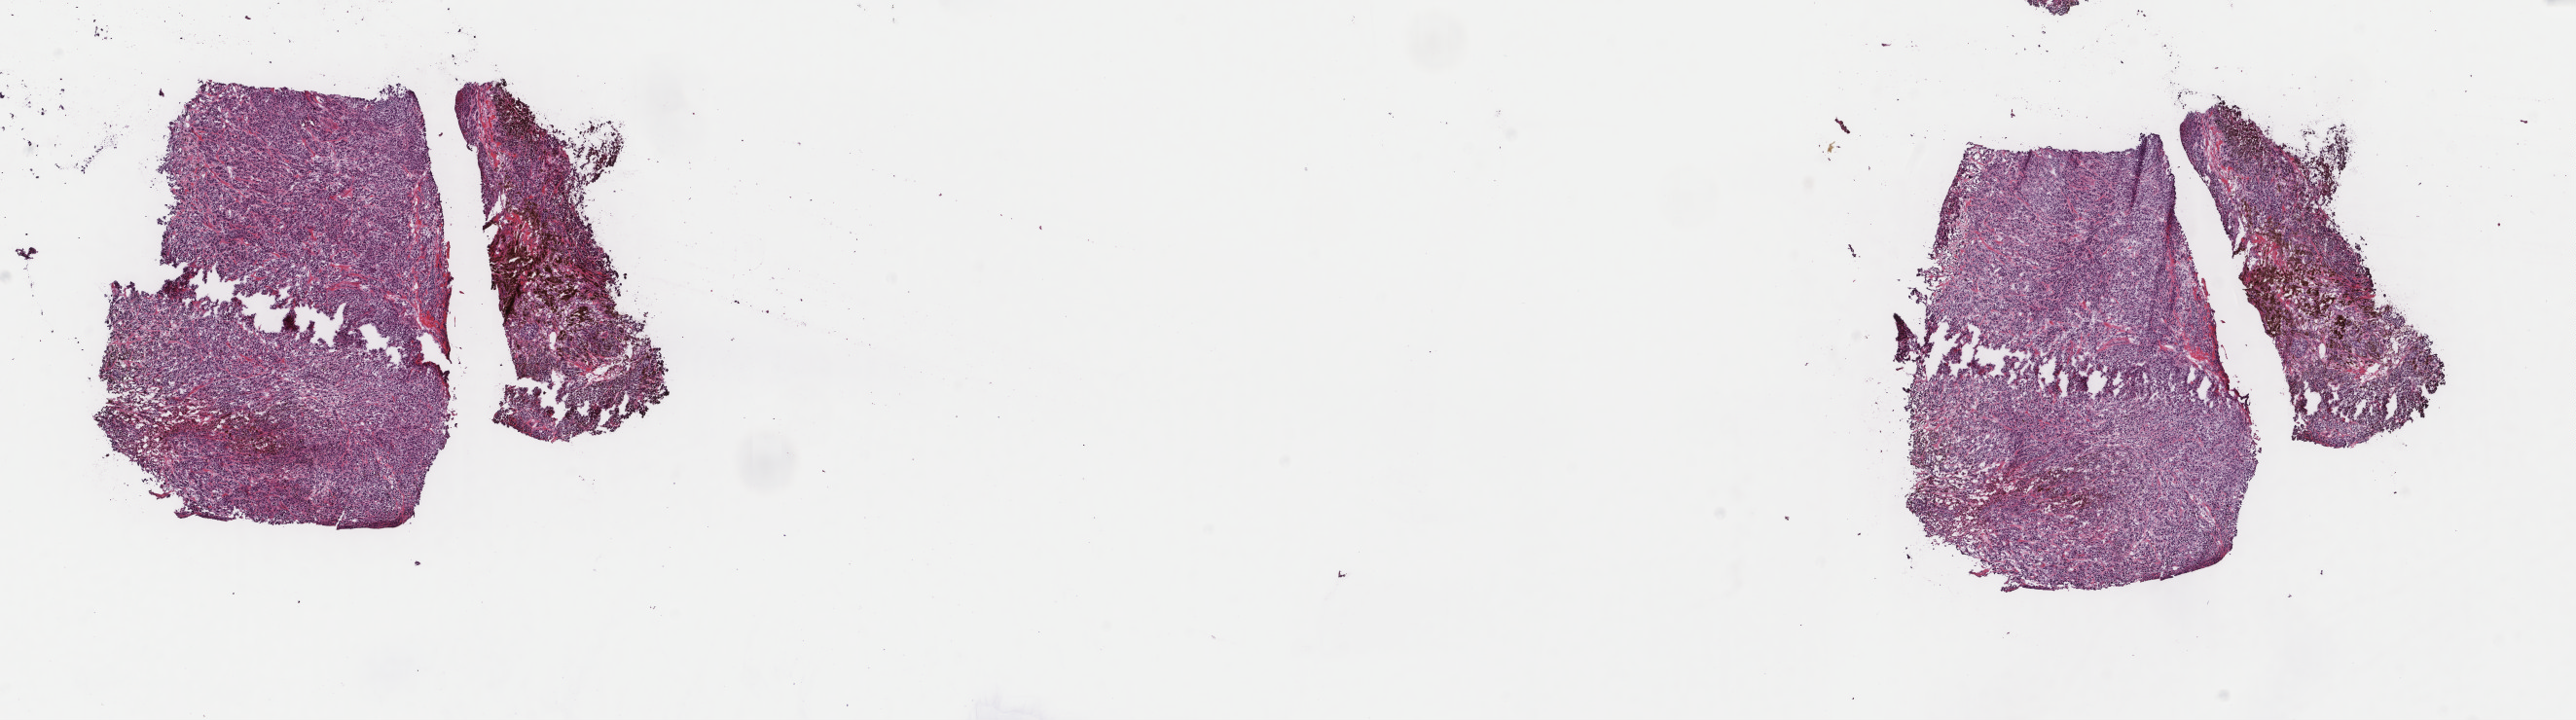
H&E whole-slide image — low-resolution overview of the scanned area, about 21.0 x 5.9 mm; frozen section from the top of the tissue portion; metastatic tumour sample. Male patient; age at initial diagnosis 53 years. Composition of this section per pathologist review: tumour cells 100%, tumour nuclei 95%, normal cells 0%, stromal cells 0%, necrosis 0%. Inflammatory infiltration, as recorded: lymphocyte infiltration 2%, monocyte infiltration 0%, neutrophil infiltration 0%.
This section: metastatic tumour tissue. Patient diagnosis: Malignant melanoma, NOS.